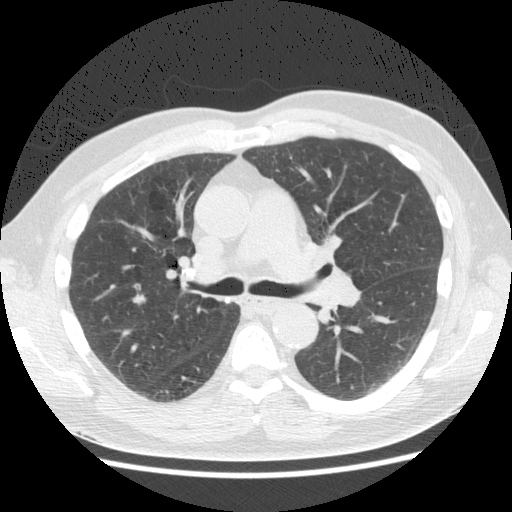
Low-dose screening chest CT, one axial slice. Lung window (W 1500 / L -600 HU). 2.5 mm slice thickness. 512 × 512 image matrix, field of view 360 × 360 mm.
Annotated regions visible in this slice (manually delineated by an expert):
- lesion 1 (tumor, upper lobe of right lung): bounding box <129,290,146,306> (left, top, right, bottom; pixels)